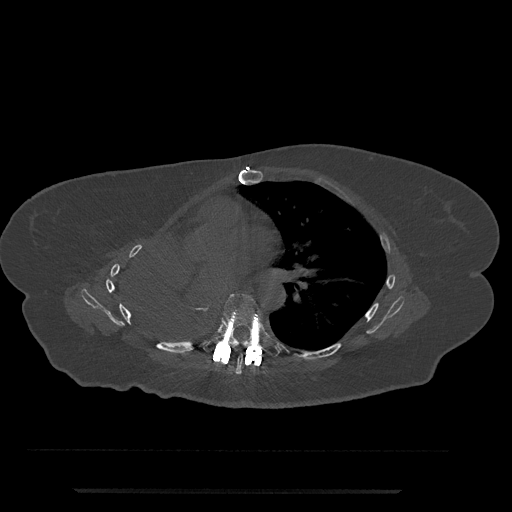
CT including the spine, one axial slice; position 458 of 797 along the scan axis; reconstruction kernel Br40s/3; bone window (W 1800 / L 400 HU); 0.5 mm slice thickness; 512 × 512 image matrix, field of view 440 × 440 mm. Patient: female, 51 years. Case-level facts recorded for this patient, not image findings: primary cancer: neuro; vertebrae with lytic lesions (as recorded): T8.
Annotated regions visible in this slice (semi-automatically segmented with operator editing):
- T6 vertebra: bounding box [x1, y1, x2, y2] px = [236, 354, 243, 374]
- T7 vertebra: [203, 293, 280, 357]